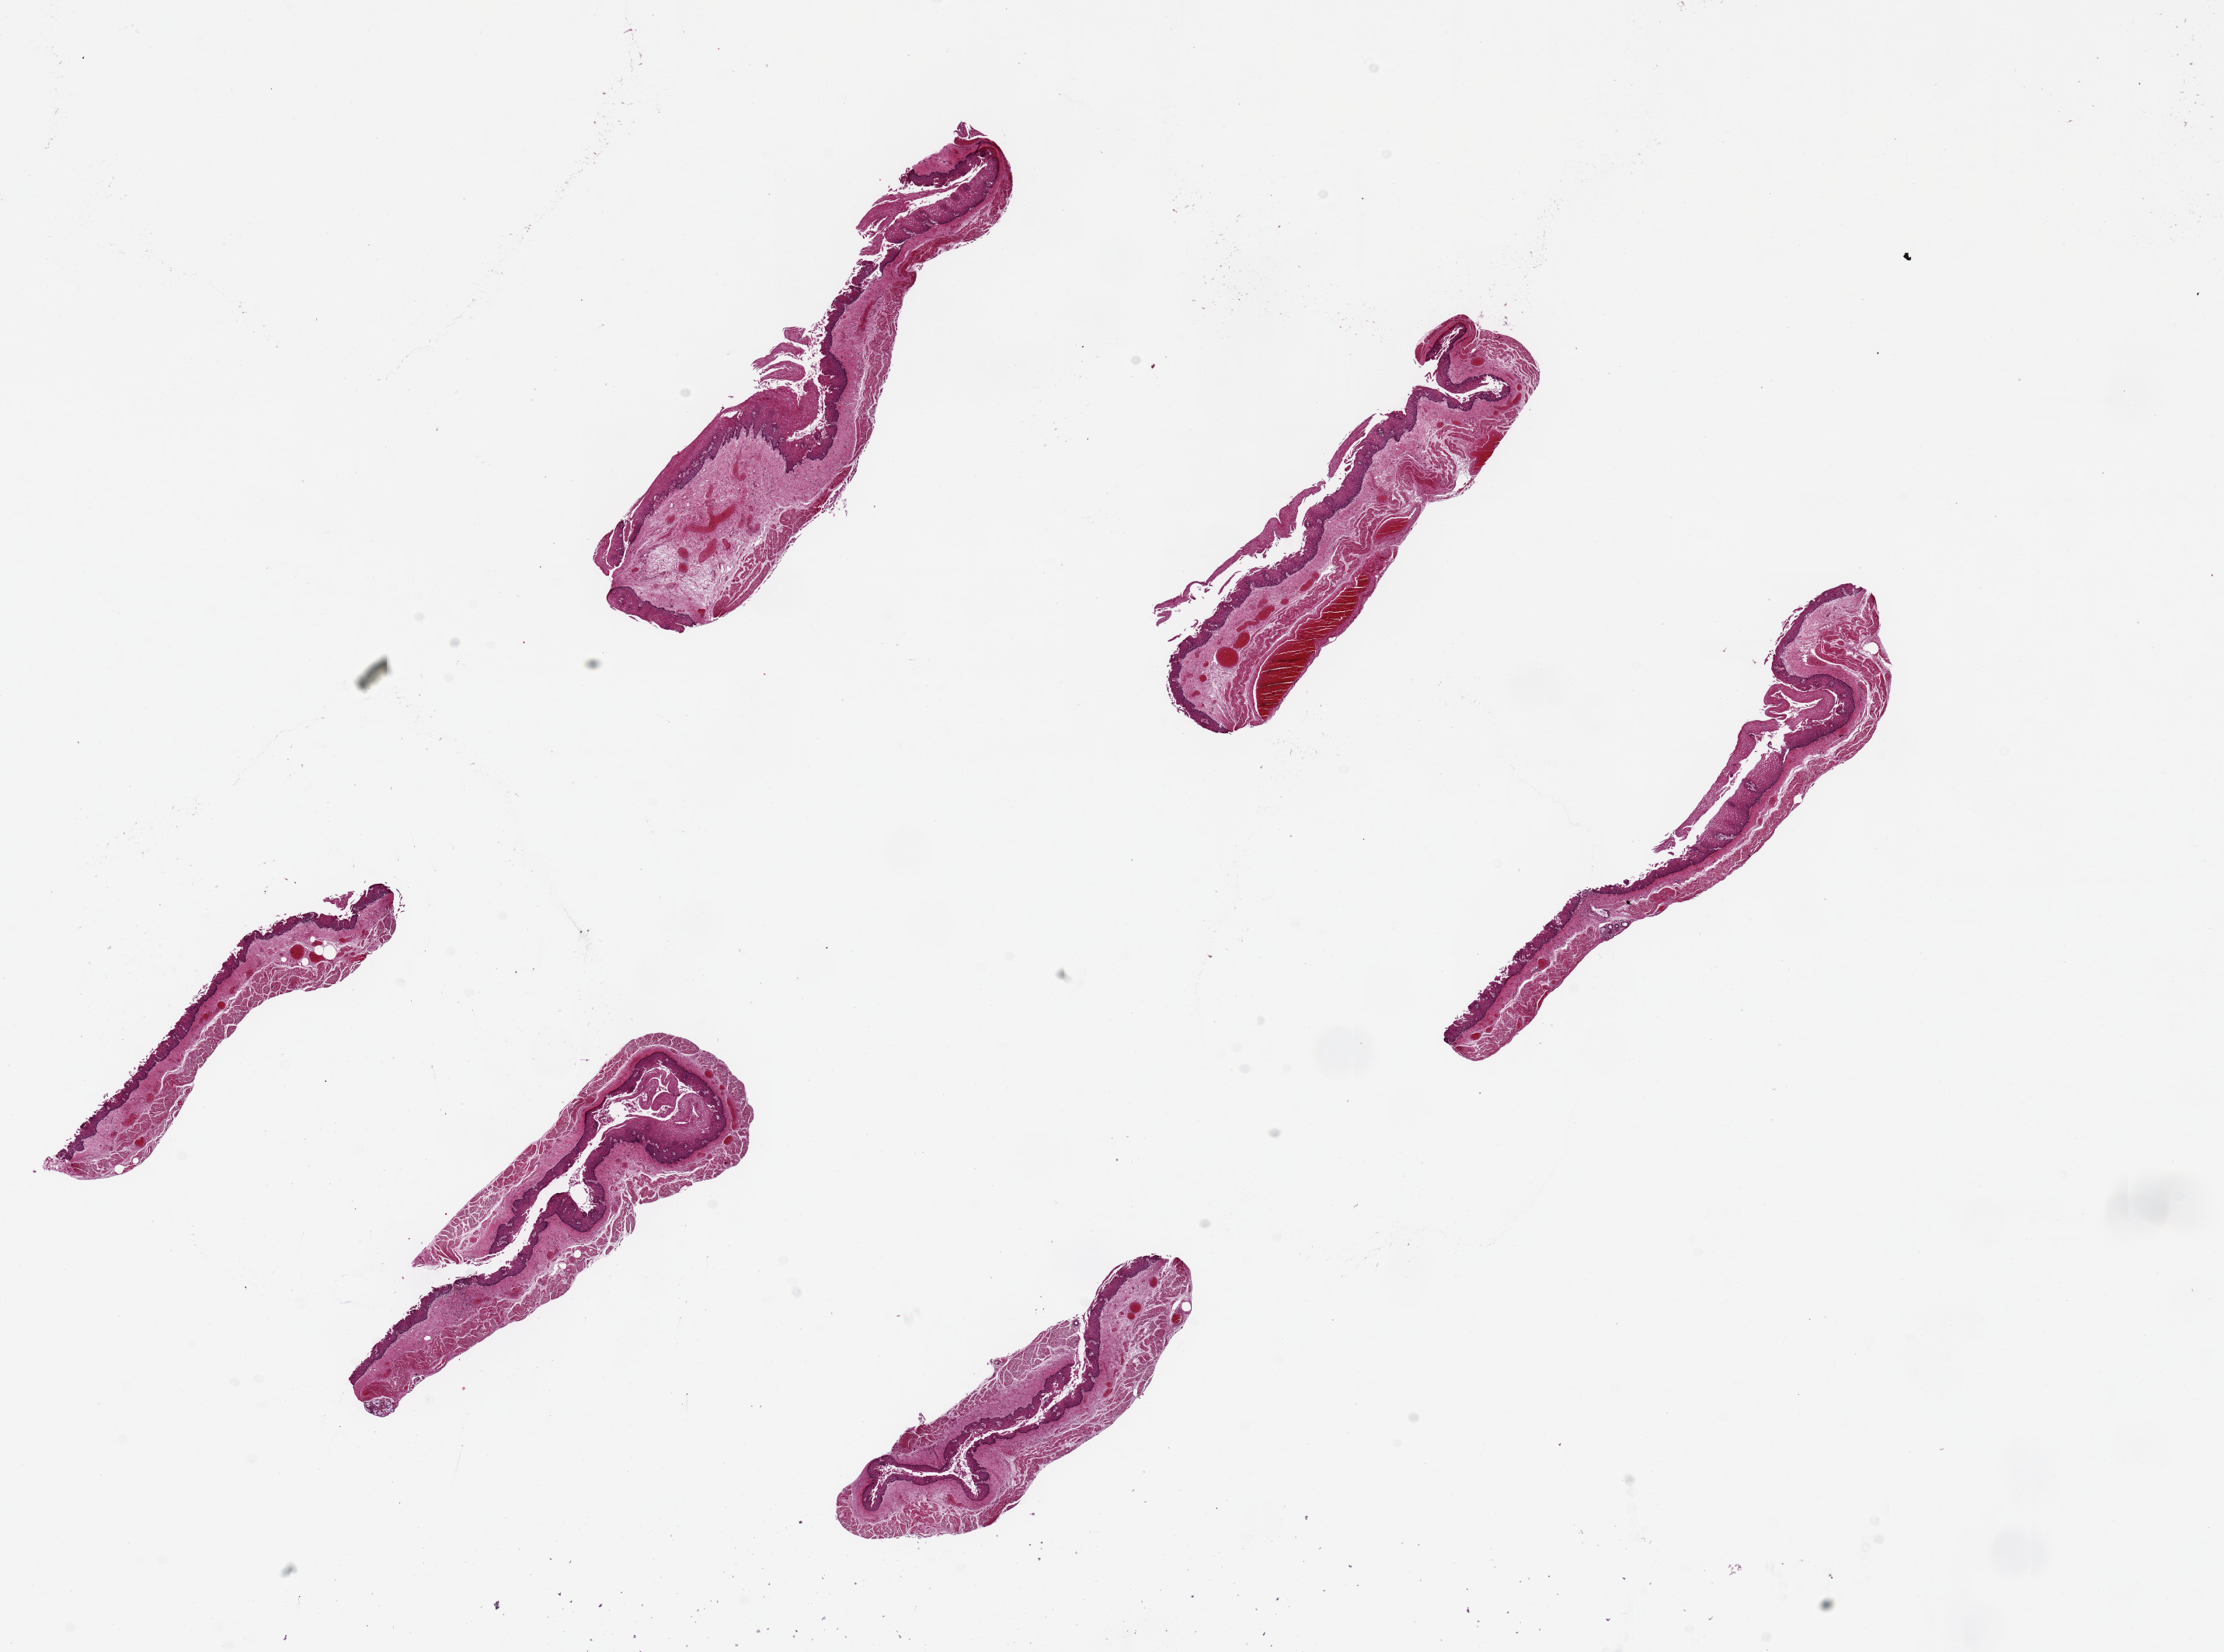
Hematoxylin and eosin (H&E) whole-slide image — a low-resolution overview of the entire scanned area, about 22.6 x 16.8 mm (slide scanned at 20x), PAXgene-fixed paraffin-embedded (PFPE) section, sampled site (target tissue): esophageal mucous membrane, tissue donor sample. Donor sex: female.
Pathologist's review note for this sample: 6 pieces, up to 6x1mm; 10-20% thickness, badly autolyzed sloughing squamous mucosa.